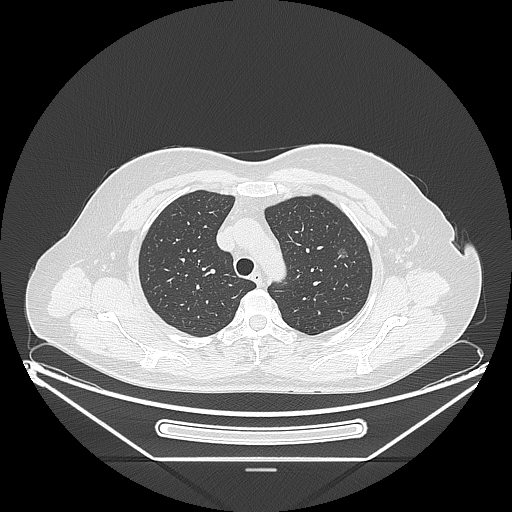
Chest CT, one axial slice; position 169 of 226 along the scan axis; 120 kVp; lung window (W 1500 / L -600 HU); 1.25 mm slice thickness; 512 × 512 image matrix, field of view 447 × 447 mm. Patient: female, 54 years. Case-level facts recorded for this patient, not image findings: clinical TNM (as recorded): T1c N0 M0; histopathological grade: G1.
Annotated regions visible in this slice (rectangle marked by the reading radiologist):
- lung tumour (recorded histology: adenocarcinoma): bounding box (x1, y1, x2, y2) in pixels: (327, 239, 365, 271)